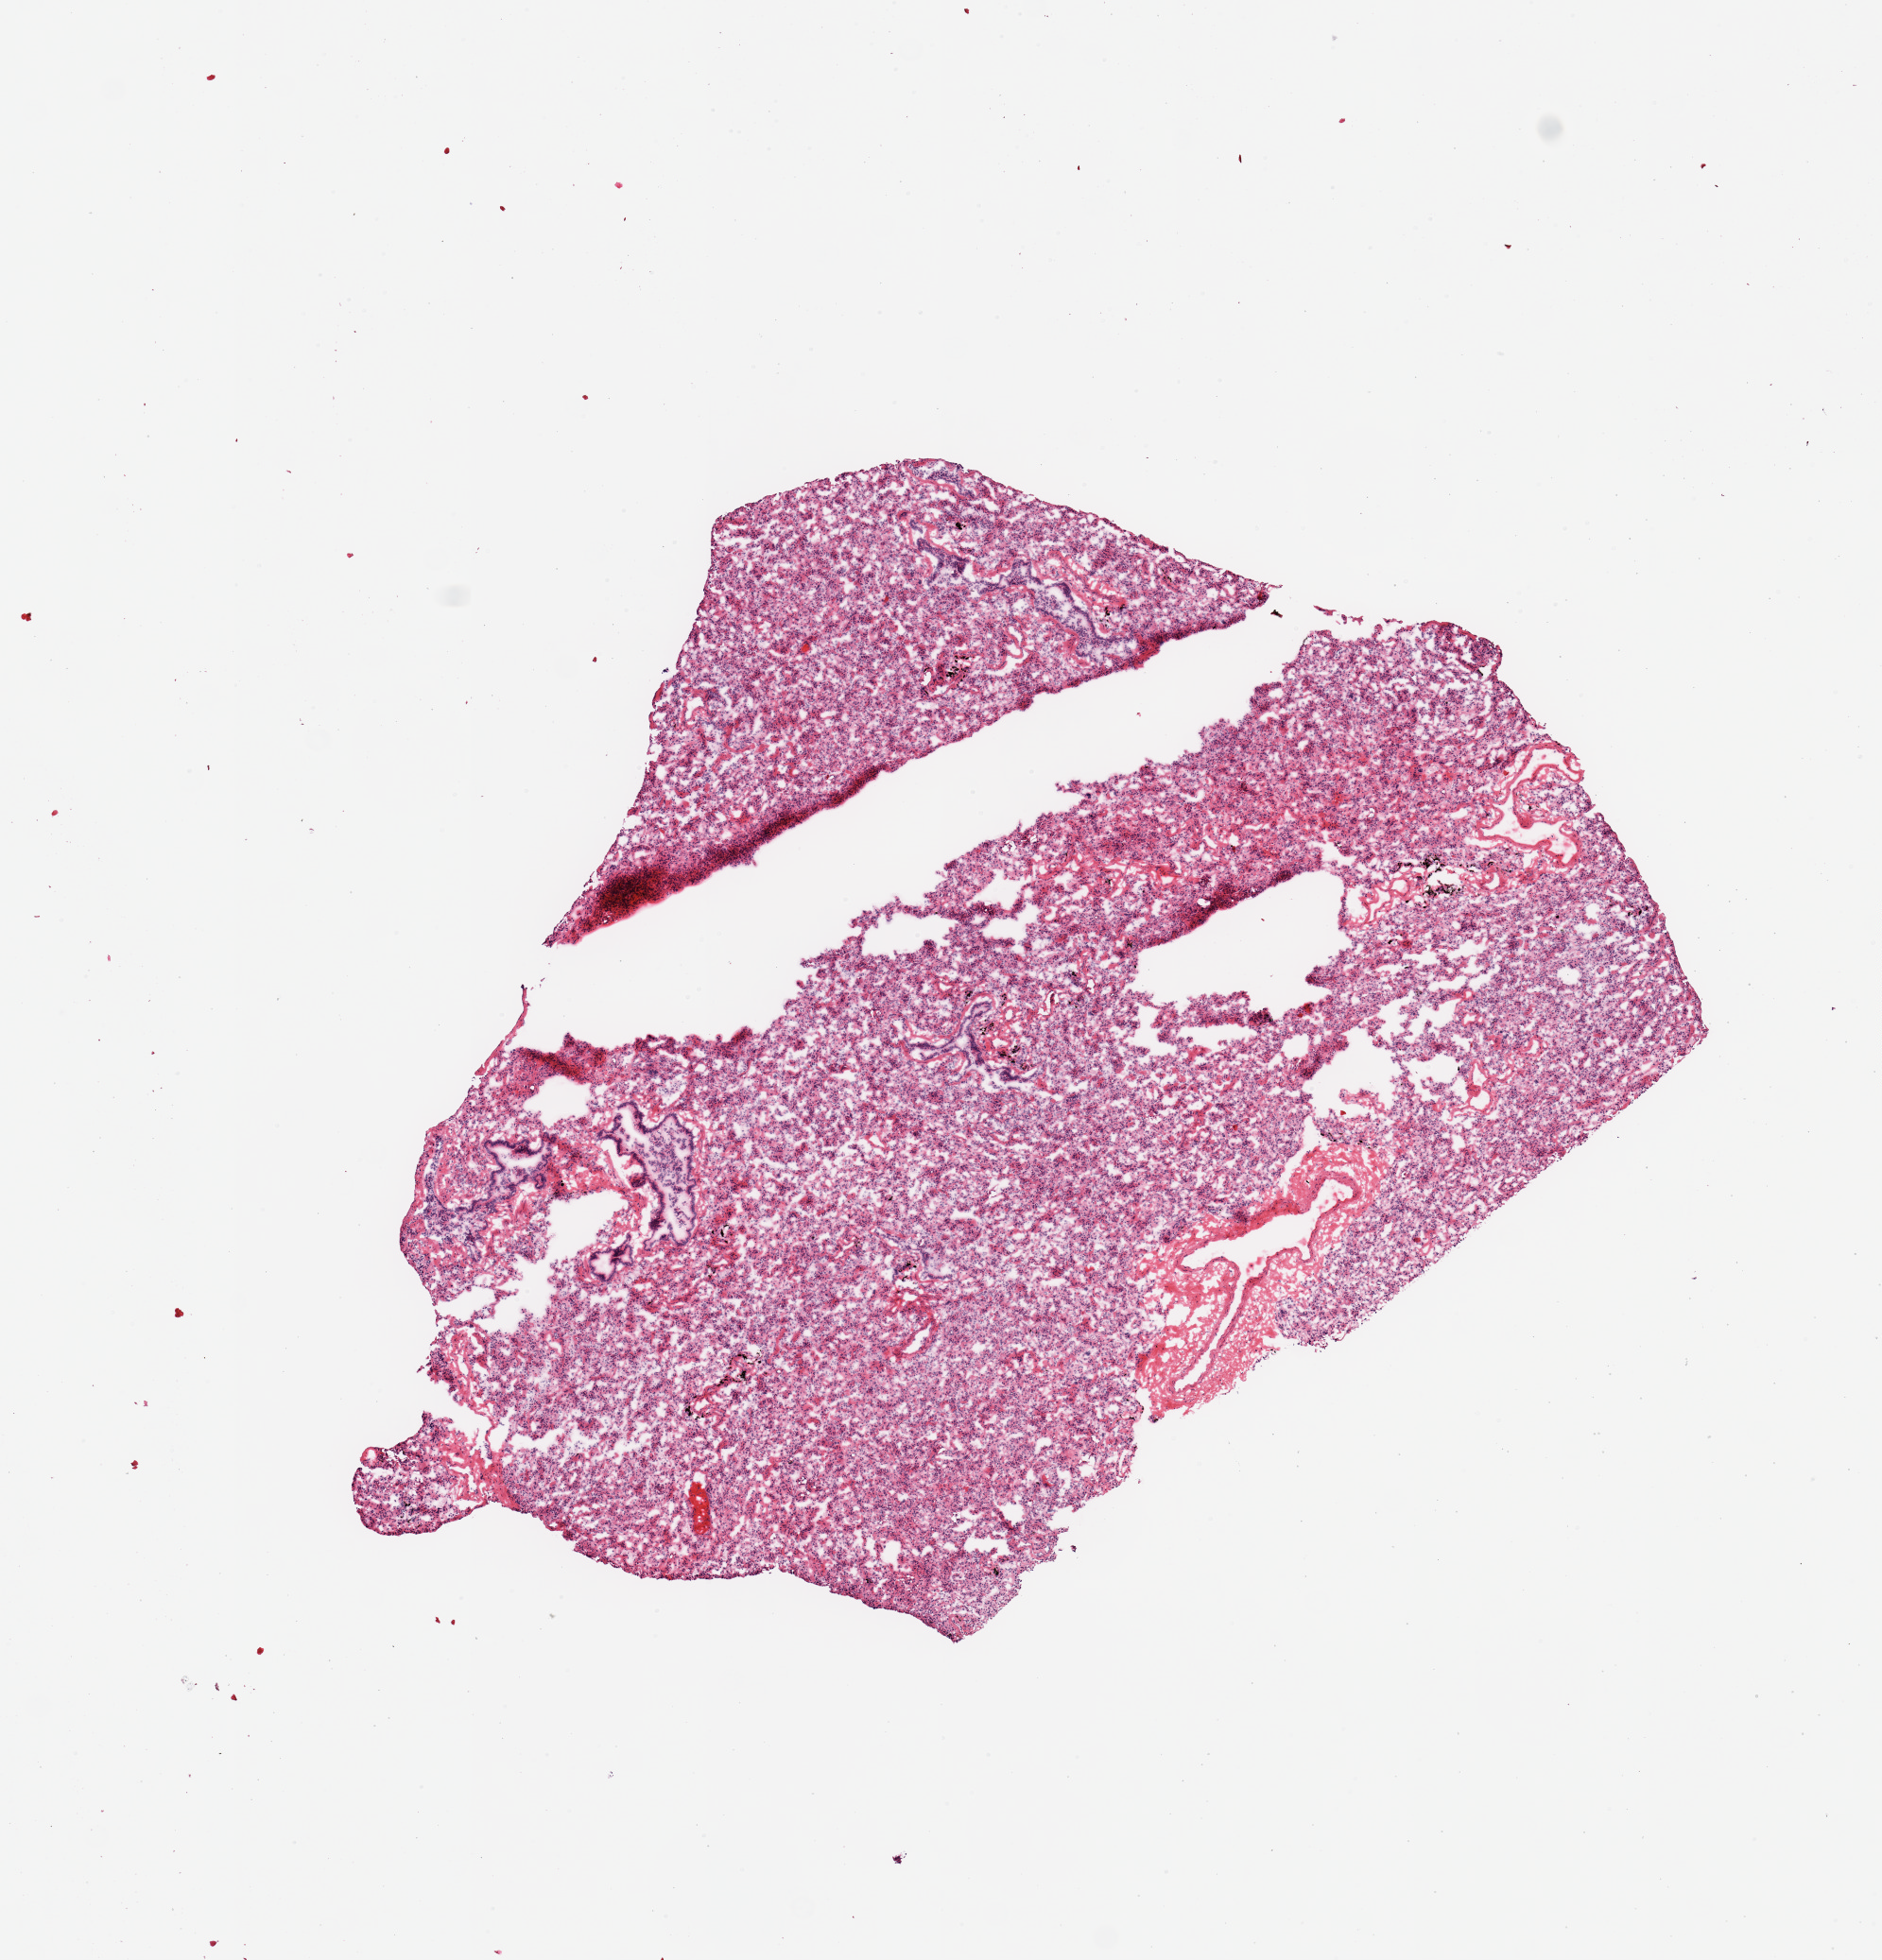
Whole-slide image, H&E stain, shown as a low-resolution overview of the whole scanned area (about 7.9 x 8.2 mm). Frozen section. Sampled site (target tissue): lung. Donor tissue sample.
* pathologist's review note for this sample: 1 piece (fragmented)